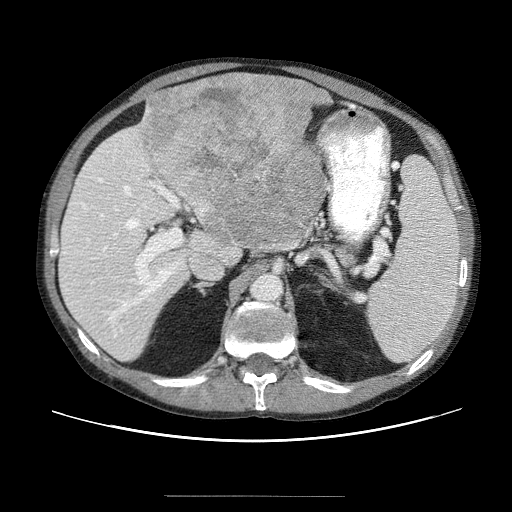
Contrast-enhanced abdominal CT (liver protocol), one axial slice; slice 28 of 69 in the series (ordered by position); reconstruction kernel STANDARD; 120 kVp; soft-tissue window (W 400 / L 40 HU); 512 × 512 image matrix, field of view 380 × 380 mm. Case-level facts recorded for this patient, not image findings: diagnosis: hepatocellular carcinoma (patient treated with transarterial chemoembolisation; whether this scan precedes or follows treatment is not stated here); TNM stage (as recorded): Stage-IVB; Child-Pugh class: B; tumour differentiation: poorly differentiated; tumour nodularity: multinodular.
Structures marked on this image (semi-automatically segmented with operator editing):
- liver parenchyma outside the tumour (the mass and vessels are separate outlines, so this box may not span the whole liver): bounding box <58,90,326,360> (left, top, right, bottom; pixels)
- mass: <135,74,330,253>
- liver vessels: <72,156,223,347>